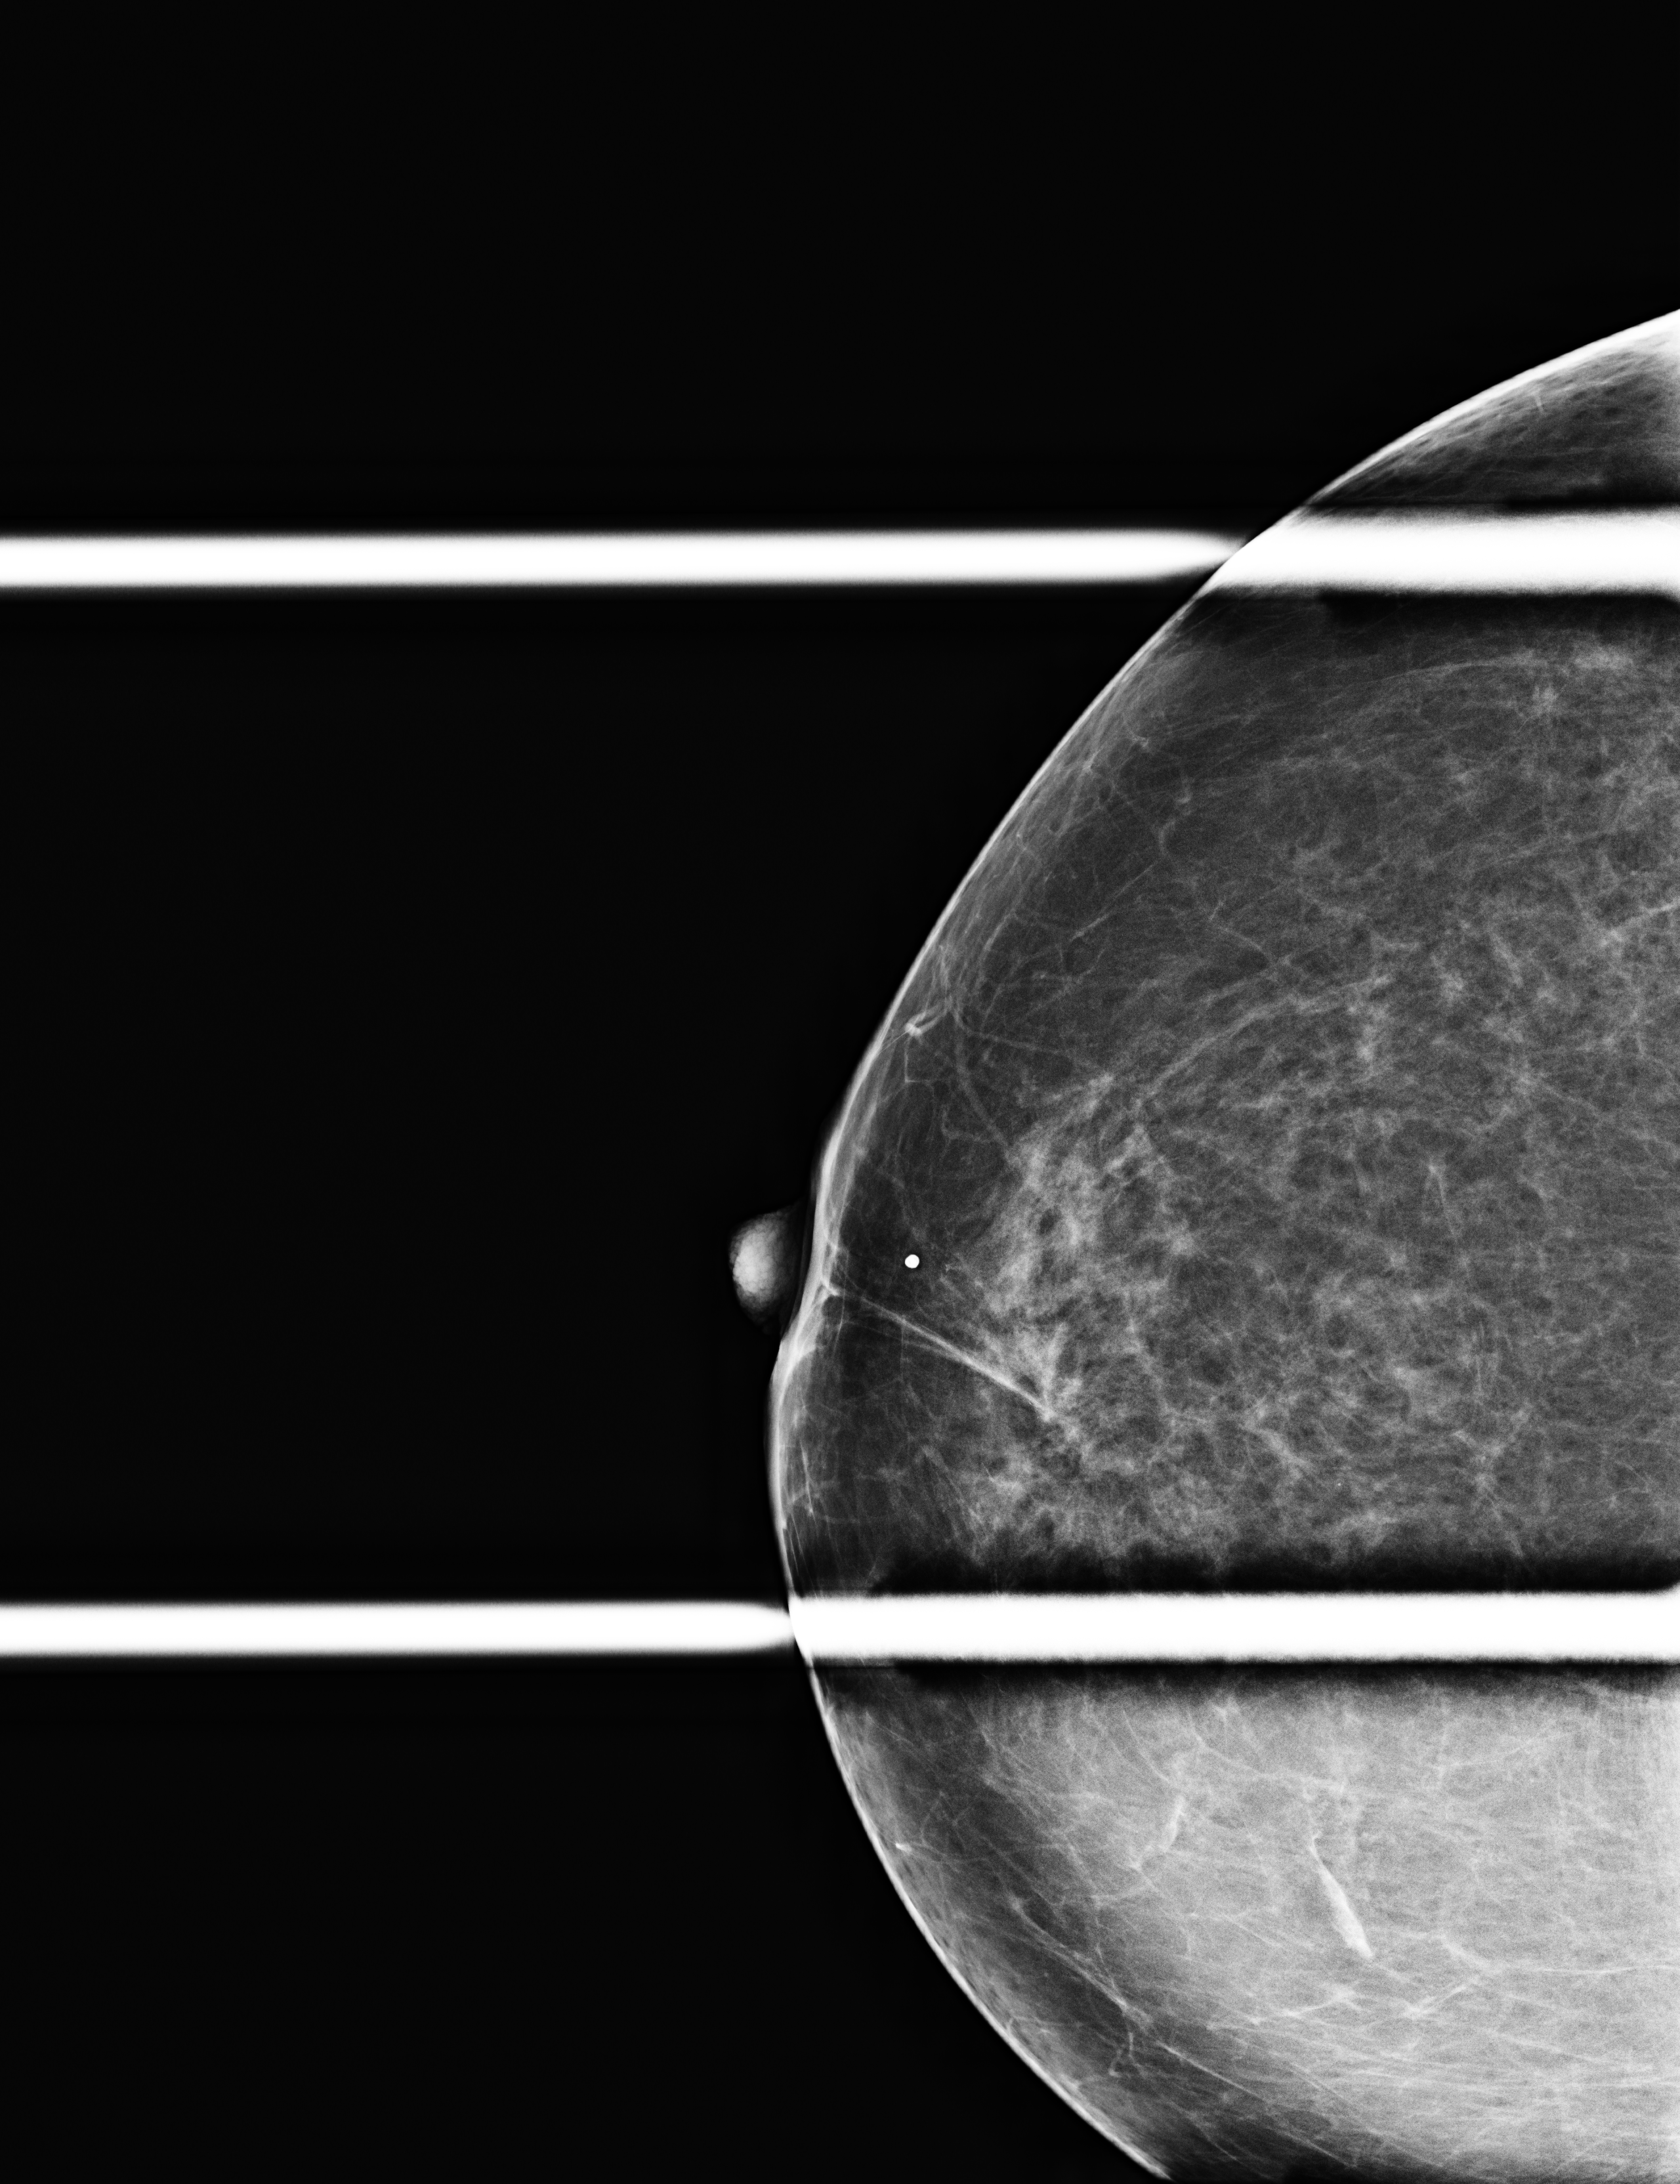
Additional work-up view; system: Selenia Dimensions. Female patient, age 75 years.
Image type: full-field digital mammogram. Breast: right. Projection: cranio-caudal projection, spot compression.